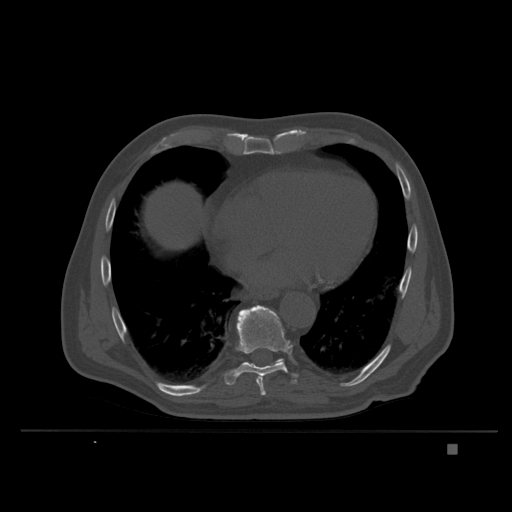
CT including the spine, one axial slice. Bone window (W 1800 / L 400 HU). 1.5 mm slice thickness. 512 × 512 image matrix, field of view 434 × 434 mm. Patient: male, 73 years. From the clinical record (not read from this slice): primary cancer: skin.
Annotated regions visible in this slice (semi-automatic segmentation, software-assisted and operator-edited):
- T10 vertebra: bounding box (x1, y1, x2, y2) in pixels: (253, 359, 282, 365)
- T9 vertebra: (223, 305, 298, 395)